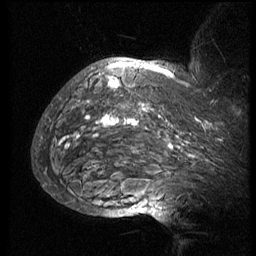
Breast MRI (dynamic contrast-enhanced), one sagittal slice. Slice 56 of 74 in the series (ordered by position). 3 images stored at this slice position (order not interpretable as contrast timing). 1.5 T. TE 4.2 ms, TR 8.9 ms. 2.5 mm slice thickness. 256 × 256 image matrix. Patient: female, 57 years. Case-level facts recorded for this patient, not image findings: setting: breast cancer imaged before/during neoadjuvant chemotherapy; receptor status: HER2-positive.
Outlined on this slice (semi-automatic segmentation, software-assisted and operator-edited):
- analysis volume of interest (the breast-tissue region the enhancement analysis was run in; not a lesion): bounding box (x1, y1, x2, y2) in pixels: (51, 67, 247, 173)
- tumour enhancement mask (voxels above the 140 % enhancement threshold inside the analysis volume of interest): (59, 67, 223, 157)